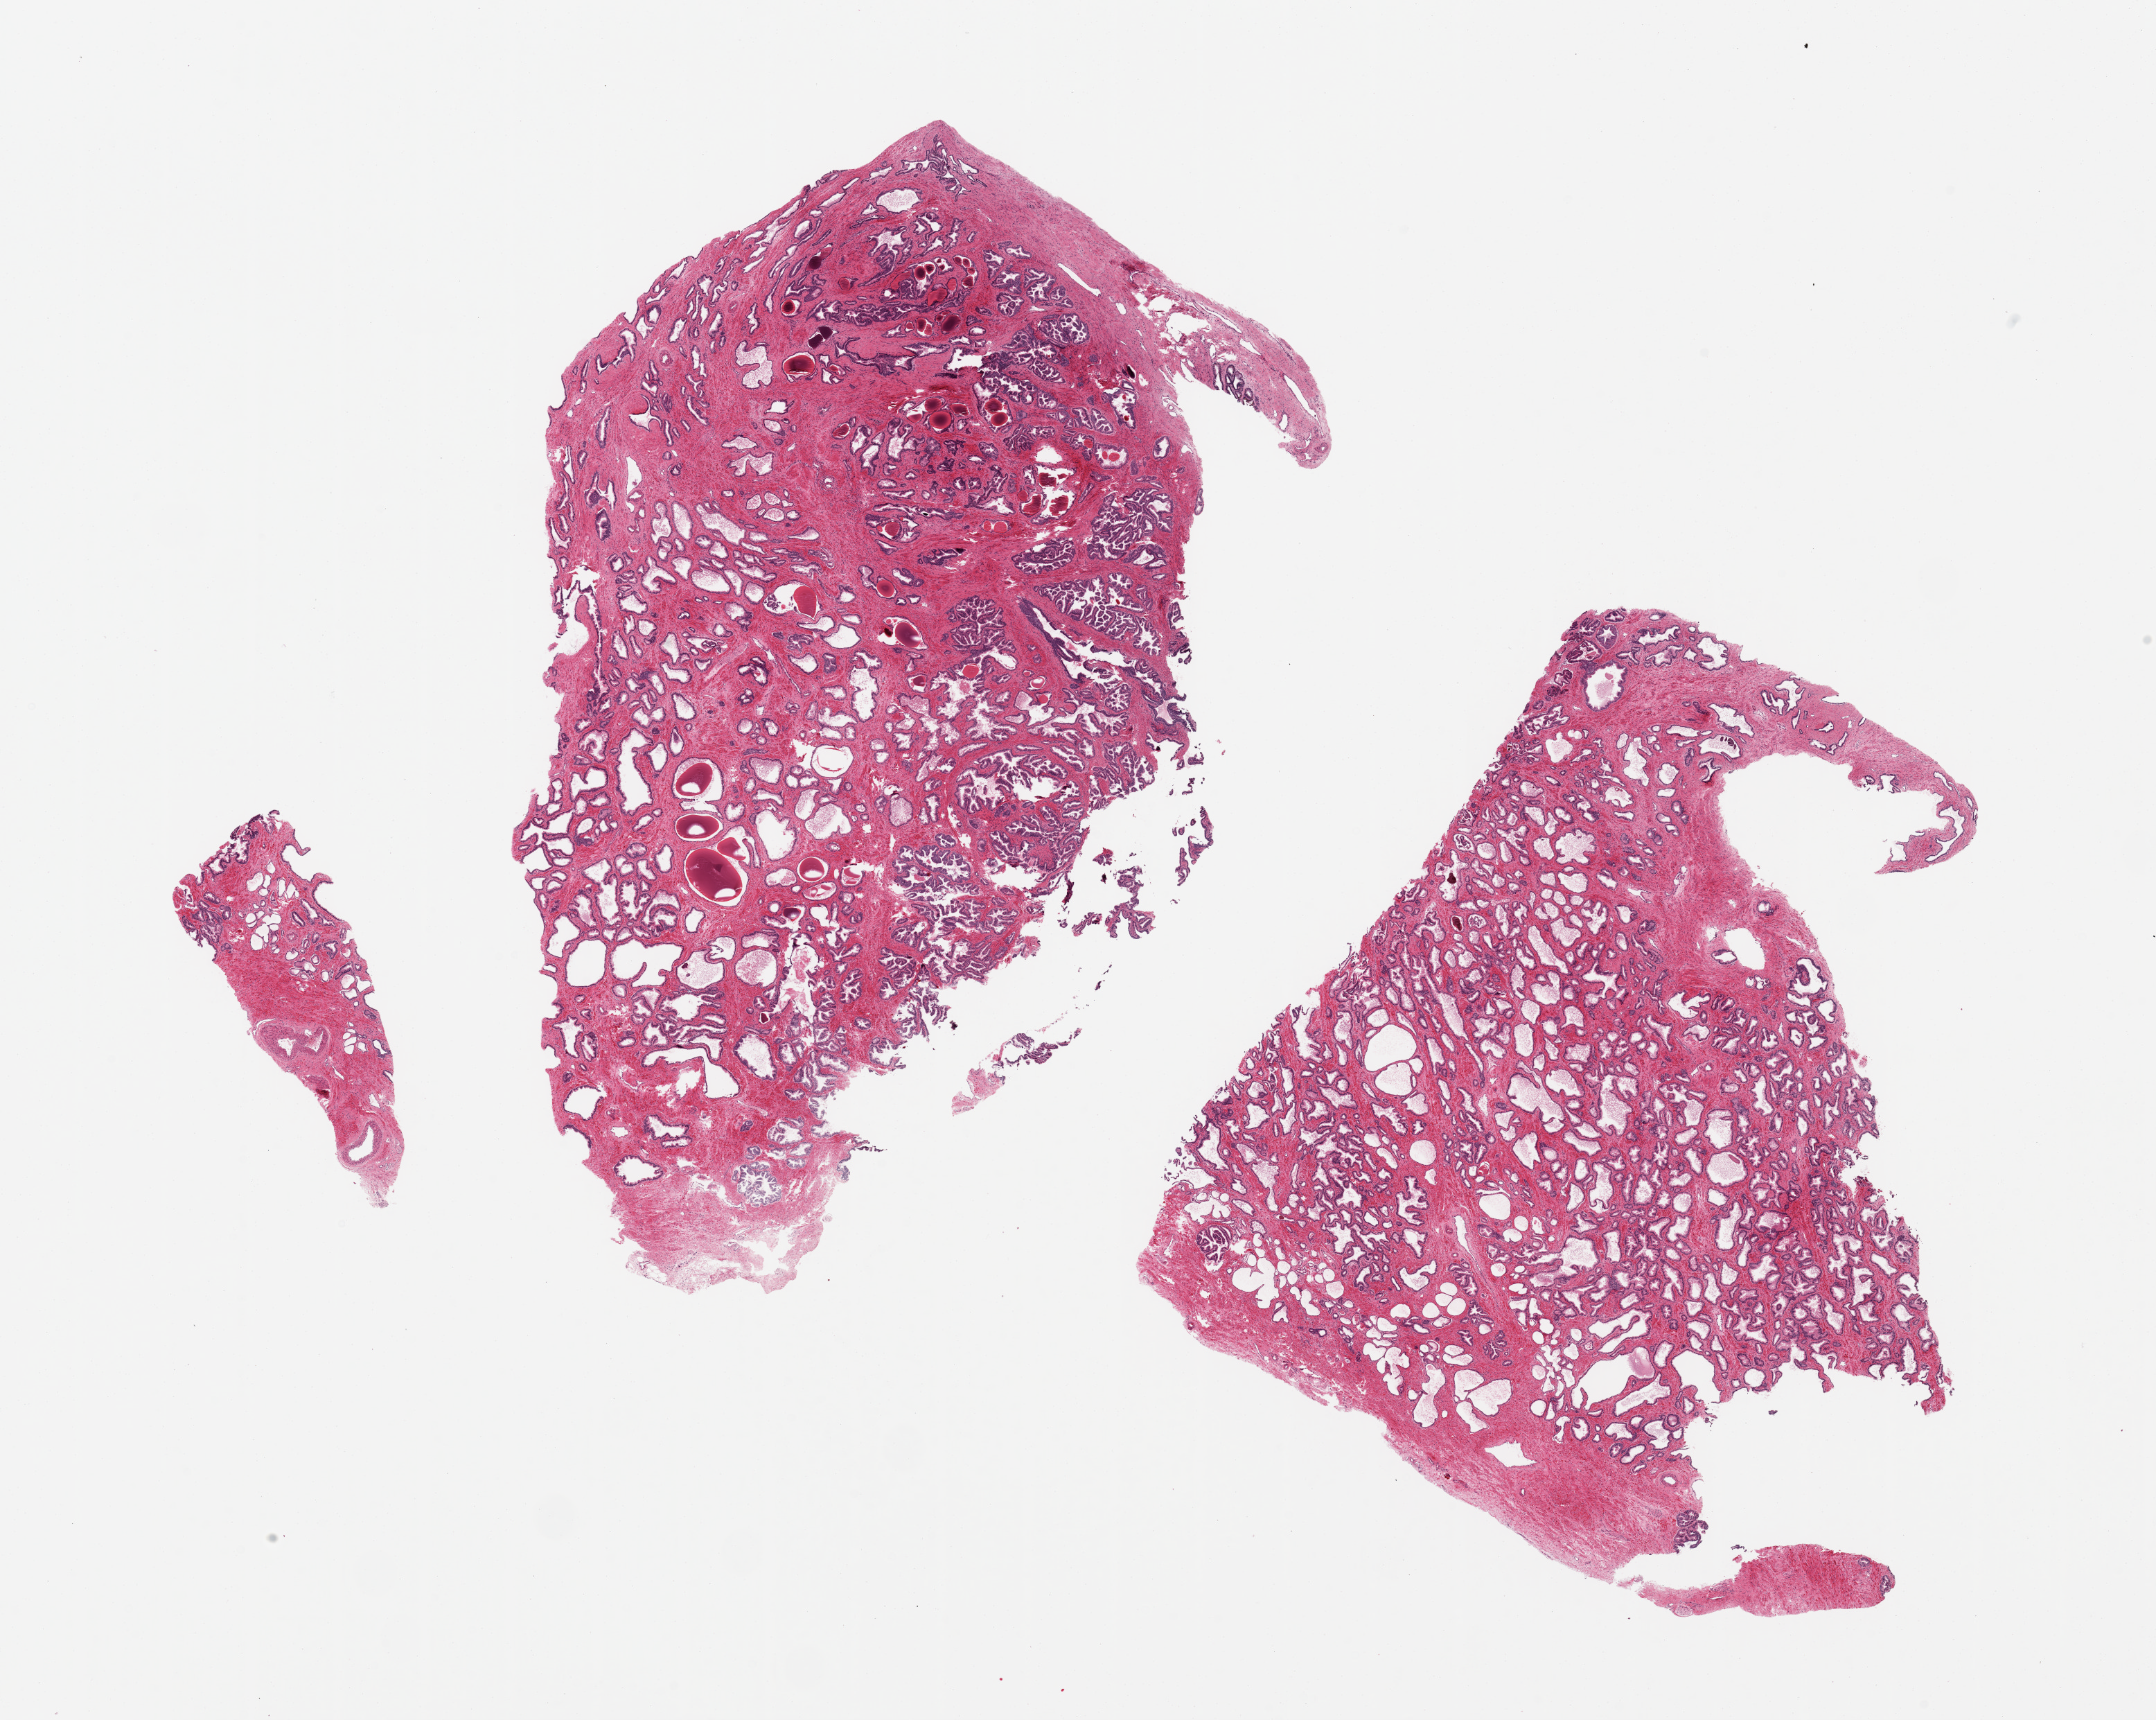
H&E whole-slide image — low-resolution overview of the scanned area, about 24.6 x 19.6 mm (acquisition: 20x scan); PAXgene-fixed, paraffin-embedded tissue; target tissue: prostate; tissue donor sample. Male donor.
Review note (as recorded): 2 pieces, NOT COLON as originally labeled. Prostate with hyperplasia.